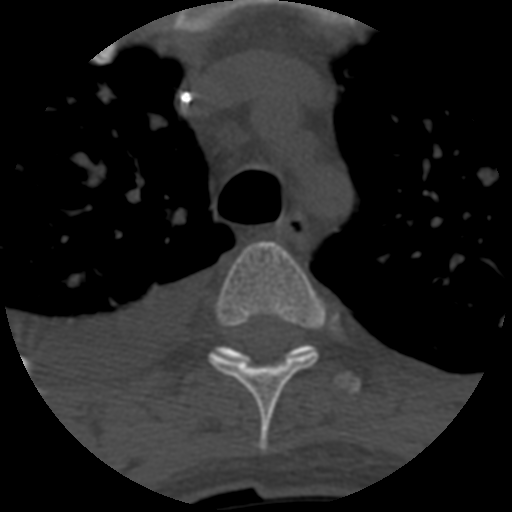
CT including the spine, one axial slice. Position 467 of 708 along the scan axis. Reconstruction kernel STANDARD. 120 kVp. One of 3 acquisitions stored at this slice position. Bone window (W 1800 / L 400 HU). 512 × 512 image matrix, field of view 160 × 160 mm. Patient age 55 years. From the clinical record (not read from this slice): primary cancer: colon.
Annotated regions visible in this slice (semi-automatically segmented with operator editing):
- T4 vertebra: box from (x=208, y=242) to (x=326, y=452) px
- T5 vertebra: (x=213, y=344)–(x=361, y=393)